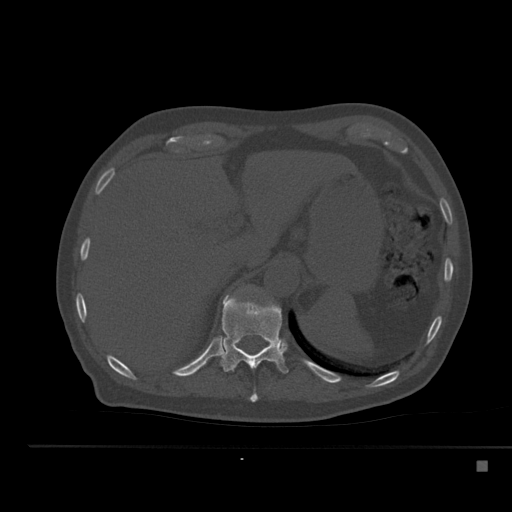
CT including the spine, one axial slice. Position 249 of 517 along the scan axis. 120 kVp. Bone window (W 1800 / L 400 HU). 1.5 mm slice thickness. 512 × 512 image matrix. Male patient, age 70 years. From the clinical record (not read from this slice): primary cancer: renal.
Annotated regions visible in this slice (semi-automatically segmented with operator editing):
- T10 vertebra: bounding box <249,389,258,402> (left, top, right, bottom; pixels)
- T11 vertebra: <220,295,289,374>